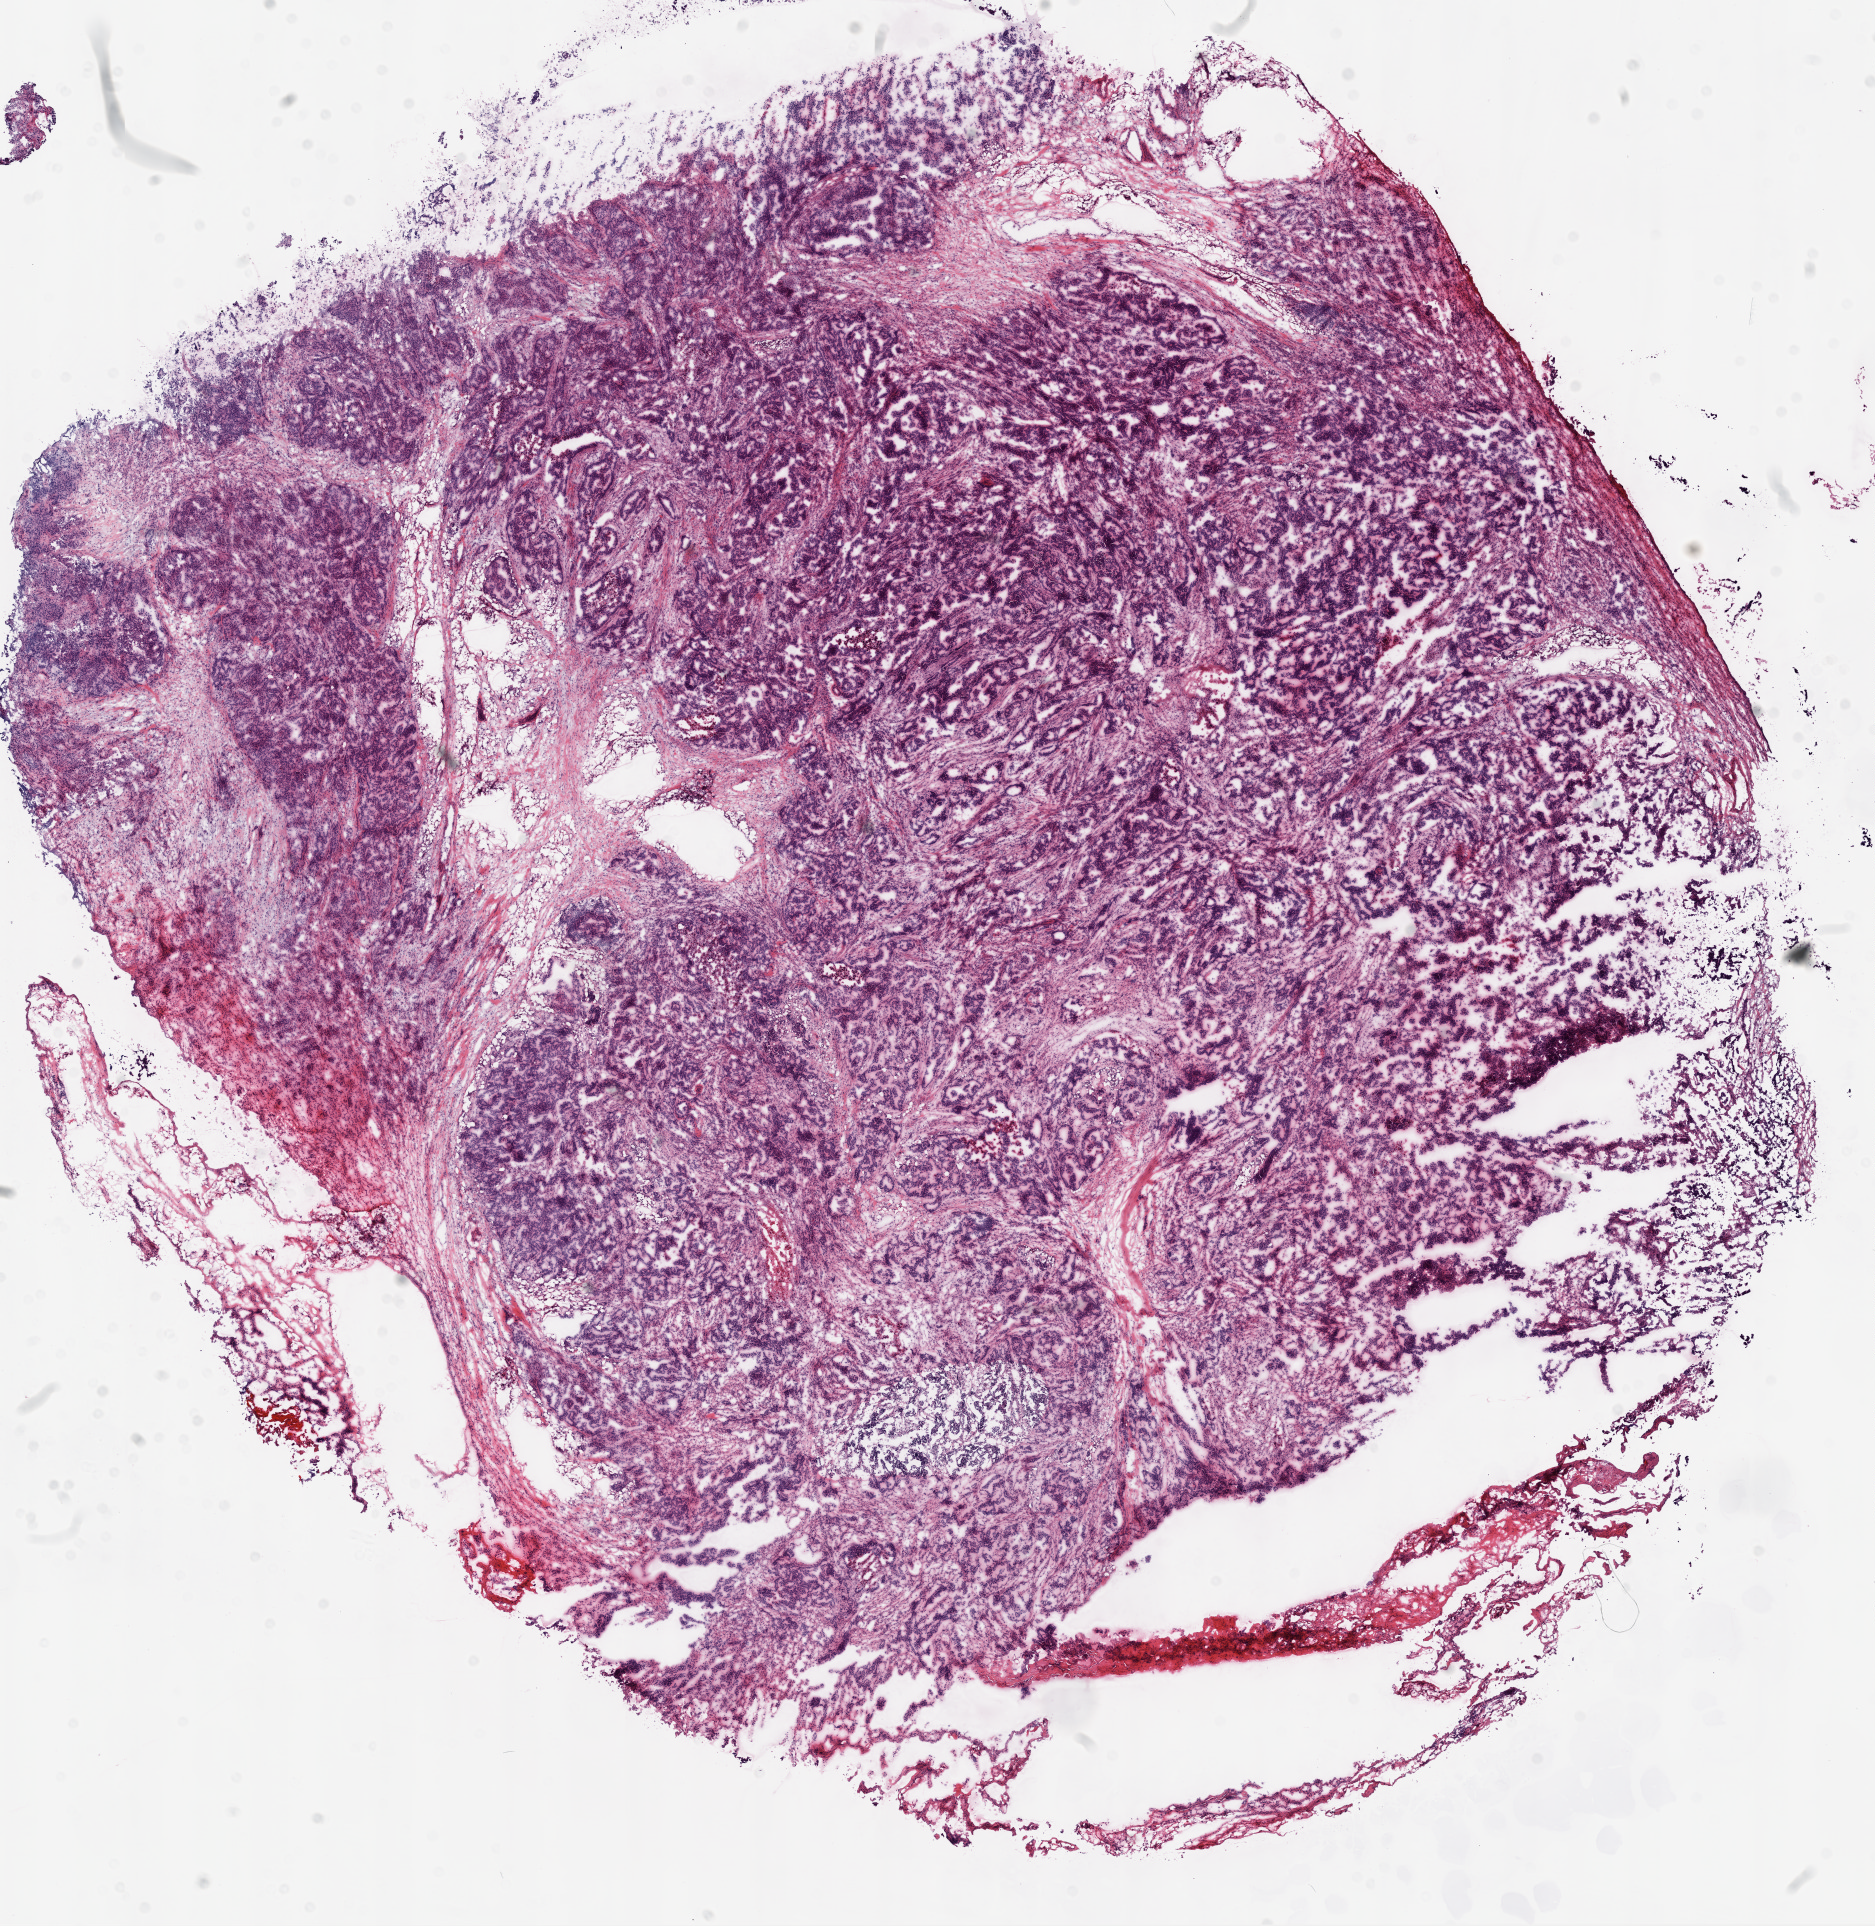
Digitized H&E-stained tissue section (whole slide), shown as a low-resolution overview of the whole scanned area (about 15.0 x 15.5 mm). Frozen section from the top of the tissue portion. Ovary, primary tumour sample. Female patient; age at initial diagnosis 76 years. Histologic grade: G2 (moderately differentiated). Pathologist review of this section (percent, as recorded): tumour cells 80%, tumour nuclei 90%, normal cells 0%, stromal cells 17%, necrosis 3%. Infiltration values recorded for this section: lymphocyte infiltration 60%, monocyte infiltration 10%, neutrophil infiltration 30%.
FIGO stage: IIIC. Laterality: right. Diagnosis: Serous cystadenocarcinoma, NOS.